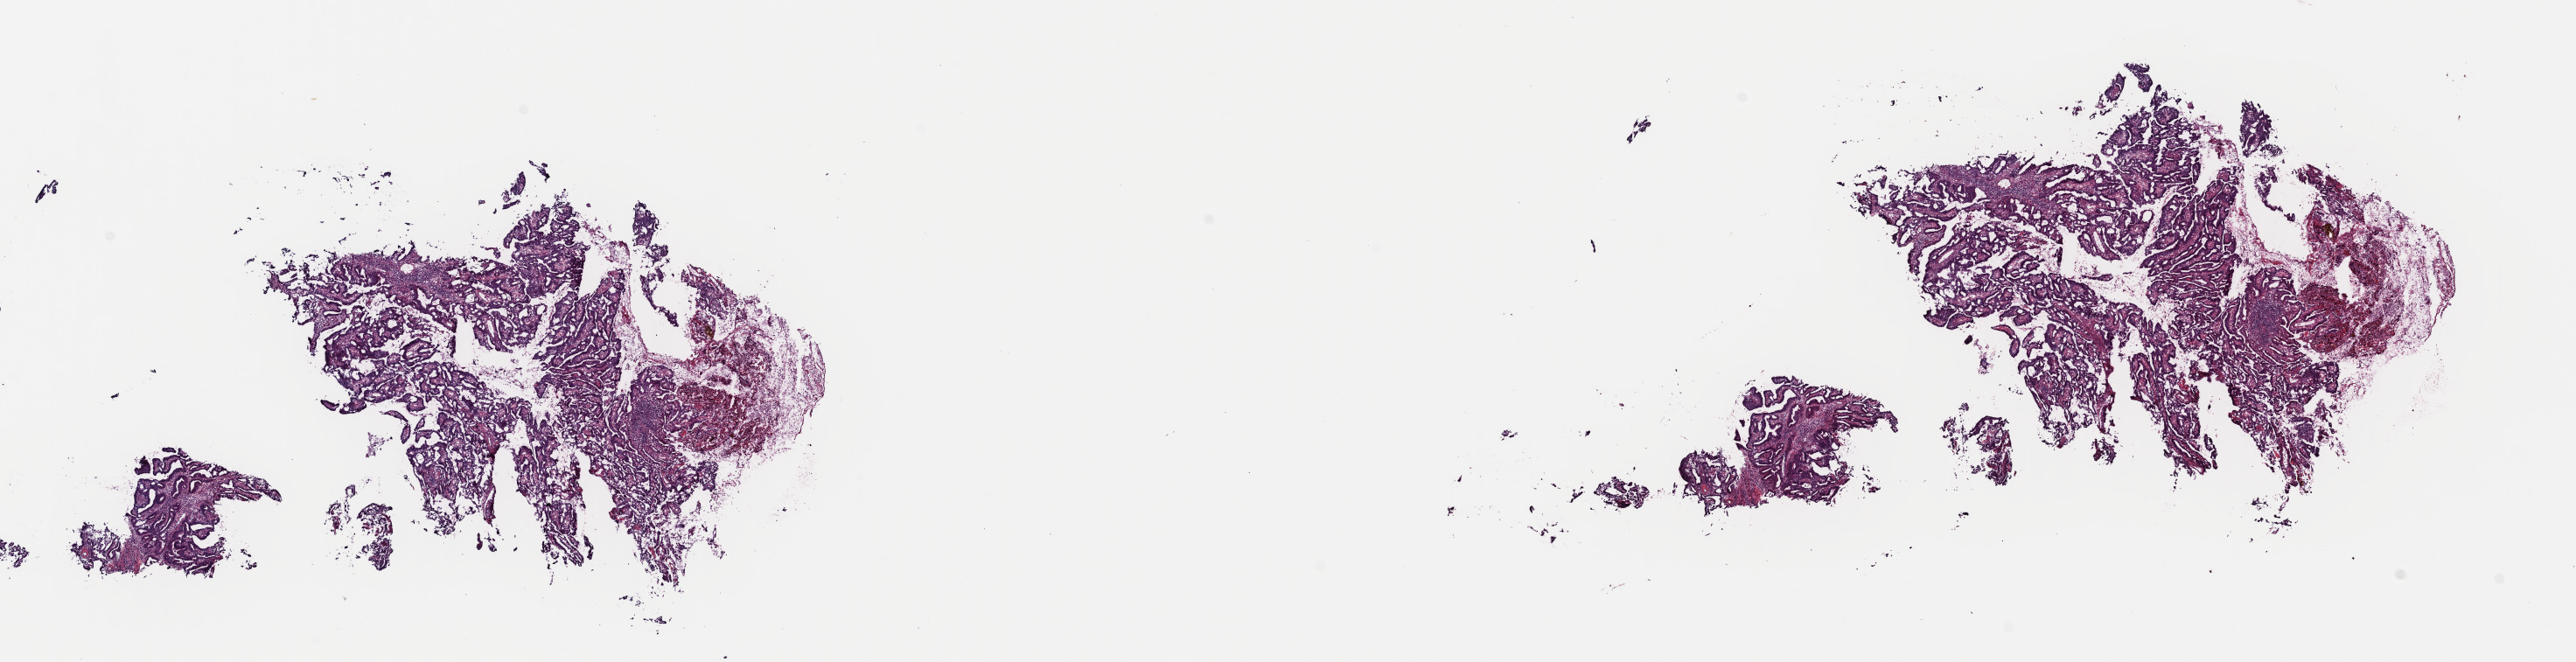
Whole-slide histology image, H&E, whole scanned area (about 23.2 x 6.0 mm, acquisition: 40x scan) shown as a low-resolution overview, frozen section from the top of the tissue portion, sample: primary tumour, cervix. Patient: female, age at initial diagnosis 45 years. Slide review estimates, as recorded: tumour cells 70%, tumour nuclei 70%.
Histologic diagnosis: Adenocarcinoma, endocervical type (cervix uteri).